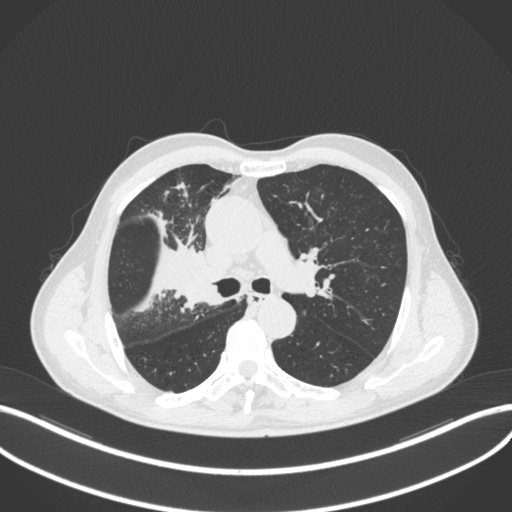
Chest CT, one axial slice; slice 313 of 490 in the series (ordered by position); reconstruction kernel B31f; 120 kVp; lung window (W 1500 / L -600 HU); 1 mm slice thickness; 512 × 512 image matrix. Patient: male, 69 years. Case-level facts recorded for this patient, not image findings: clinical TNM (as recorded): T2a N0 M0.
Annotated regions visible in this slice (bounding box drawn by a radiologist):
- lung tumour (recorded histology: adenocarcinoma): bounding box <171,261,216,314> (left, top, right, bottom; pixels)